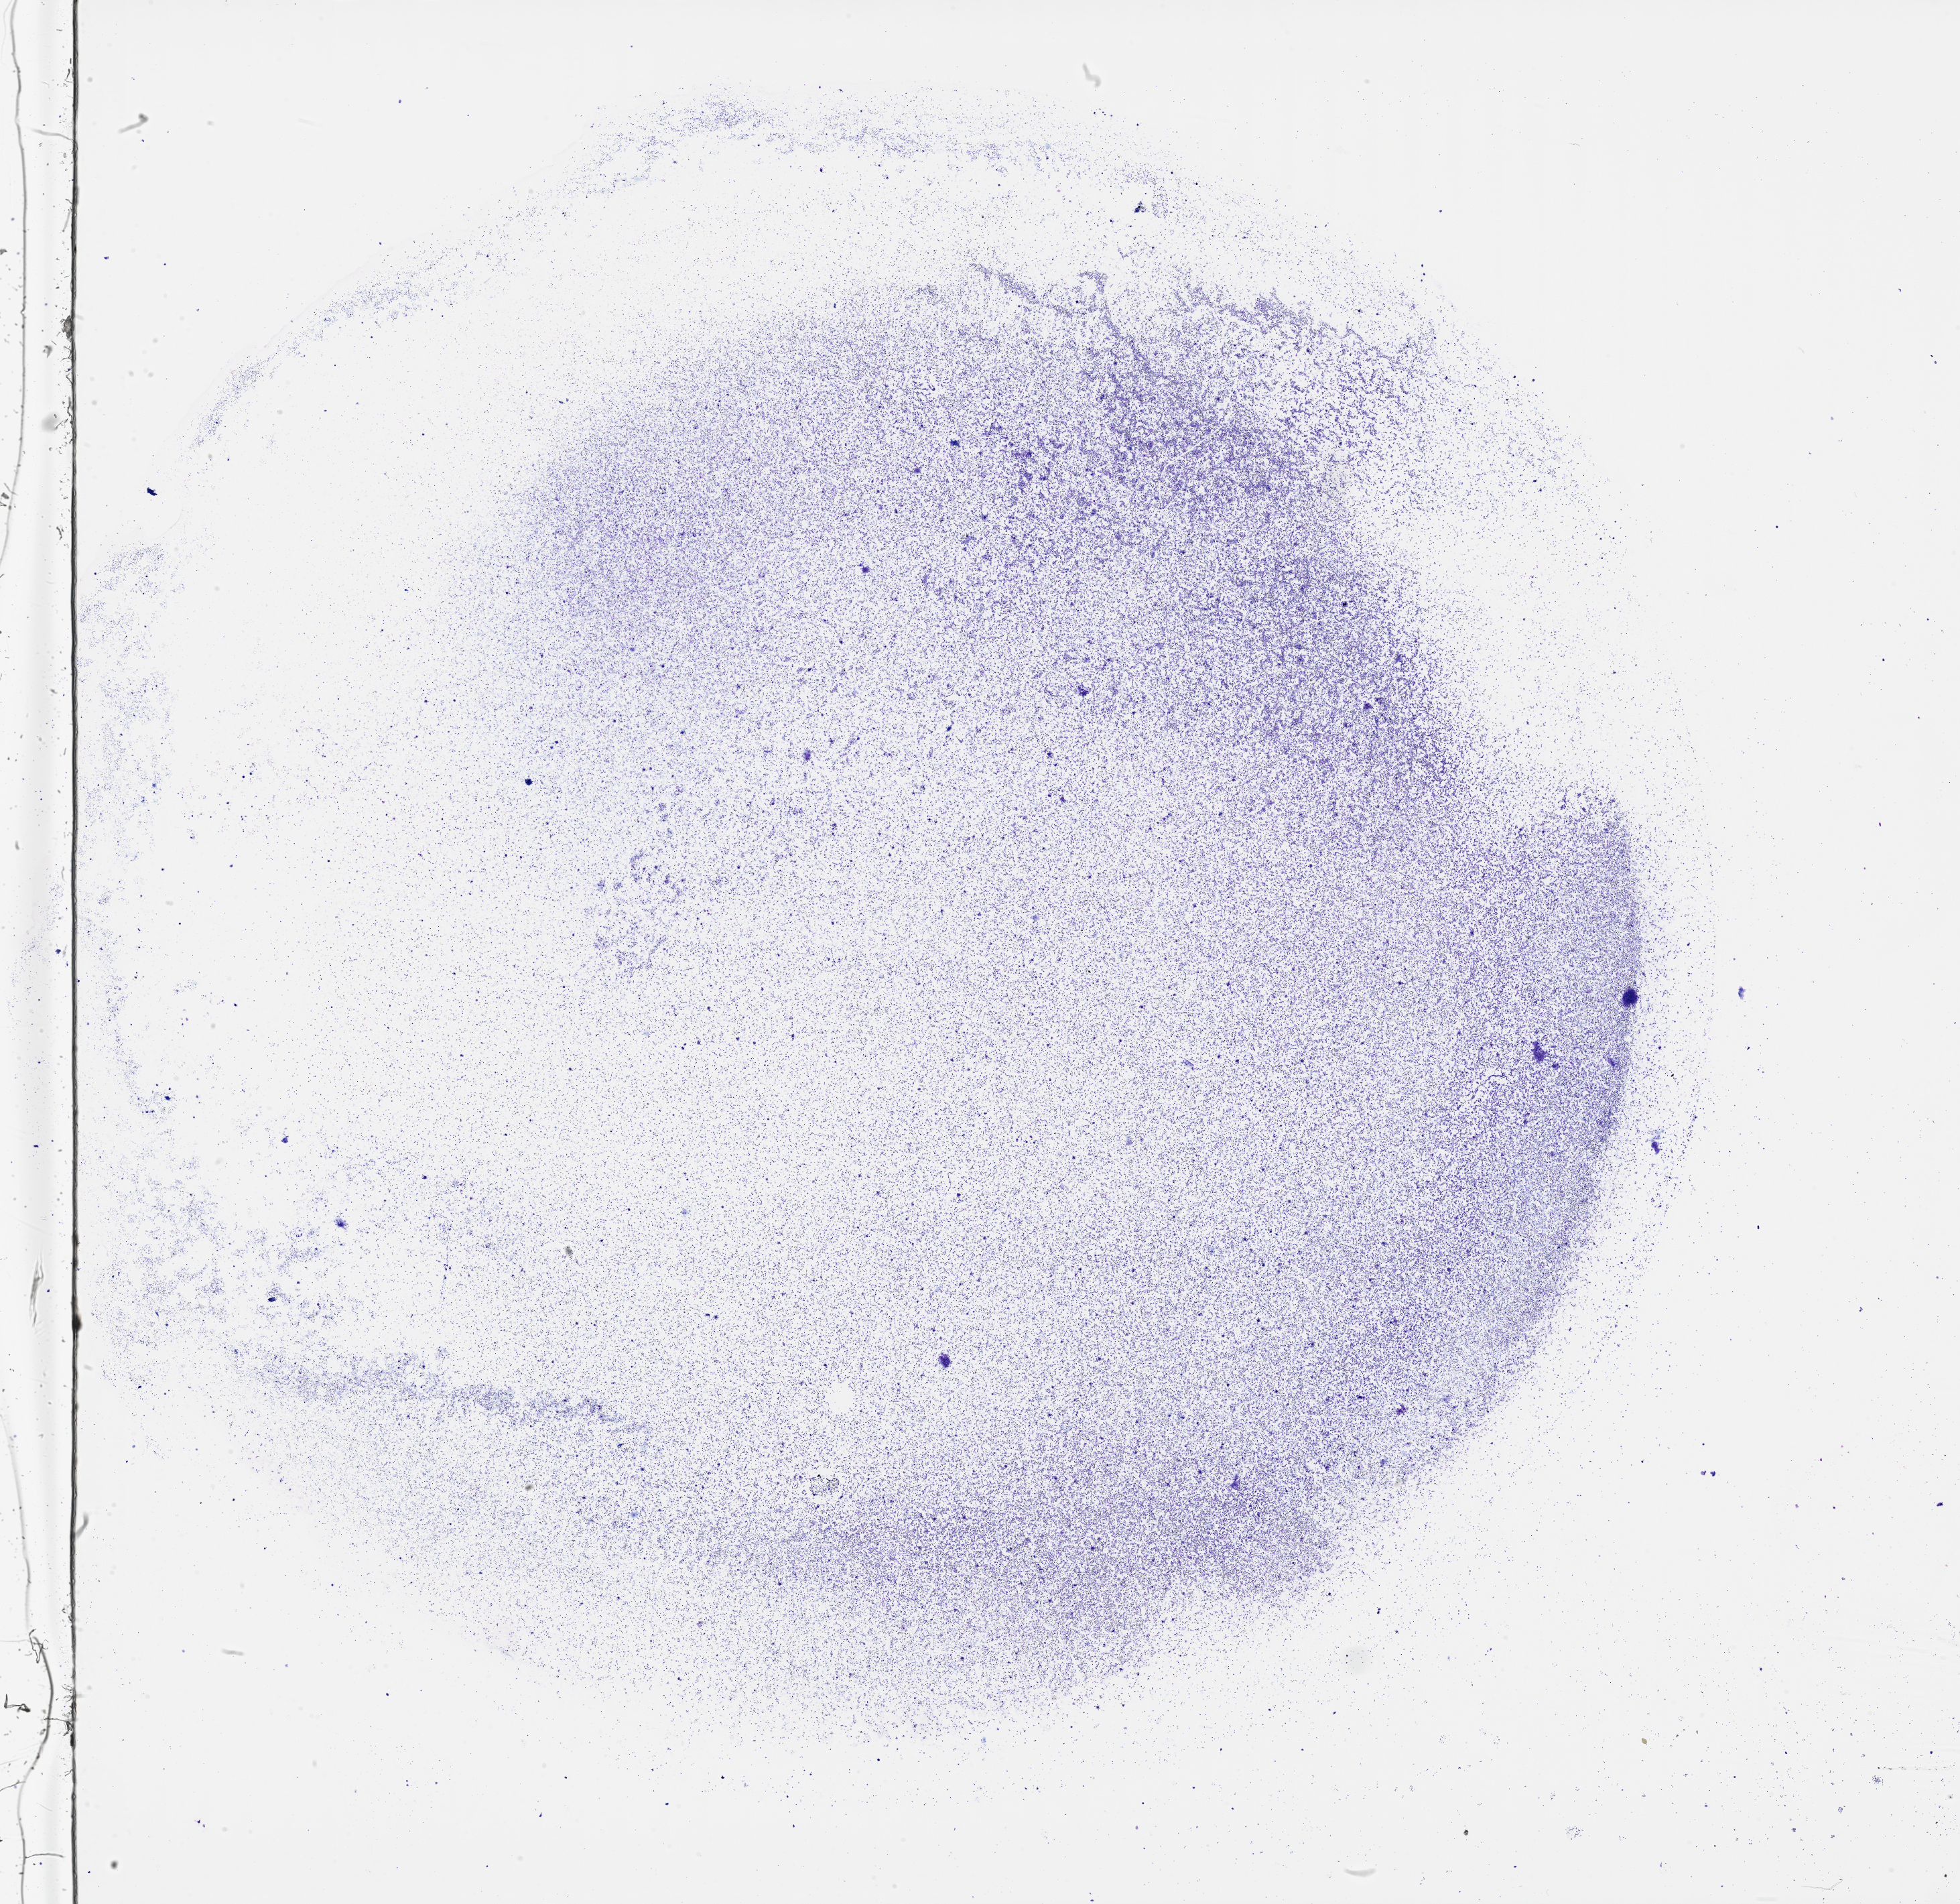
Whole-slide histology image, Hematoxylin and eosin (H&E) stained, whole scanned area (about 23.6 x 22.9 mm) shown as a low-resolution overview; bone marrow (leukaemic) sample. 78-year-old female patient. Blasts: 30%.
Diagnosis: Acute Myeloid Leukemia. FAB classification: M4. WHO classification: Acute myelomonocytic leukemia.